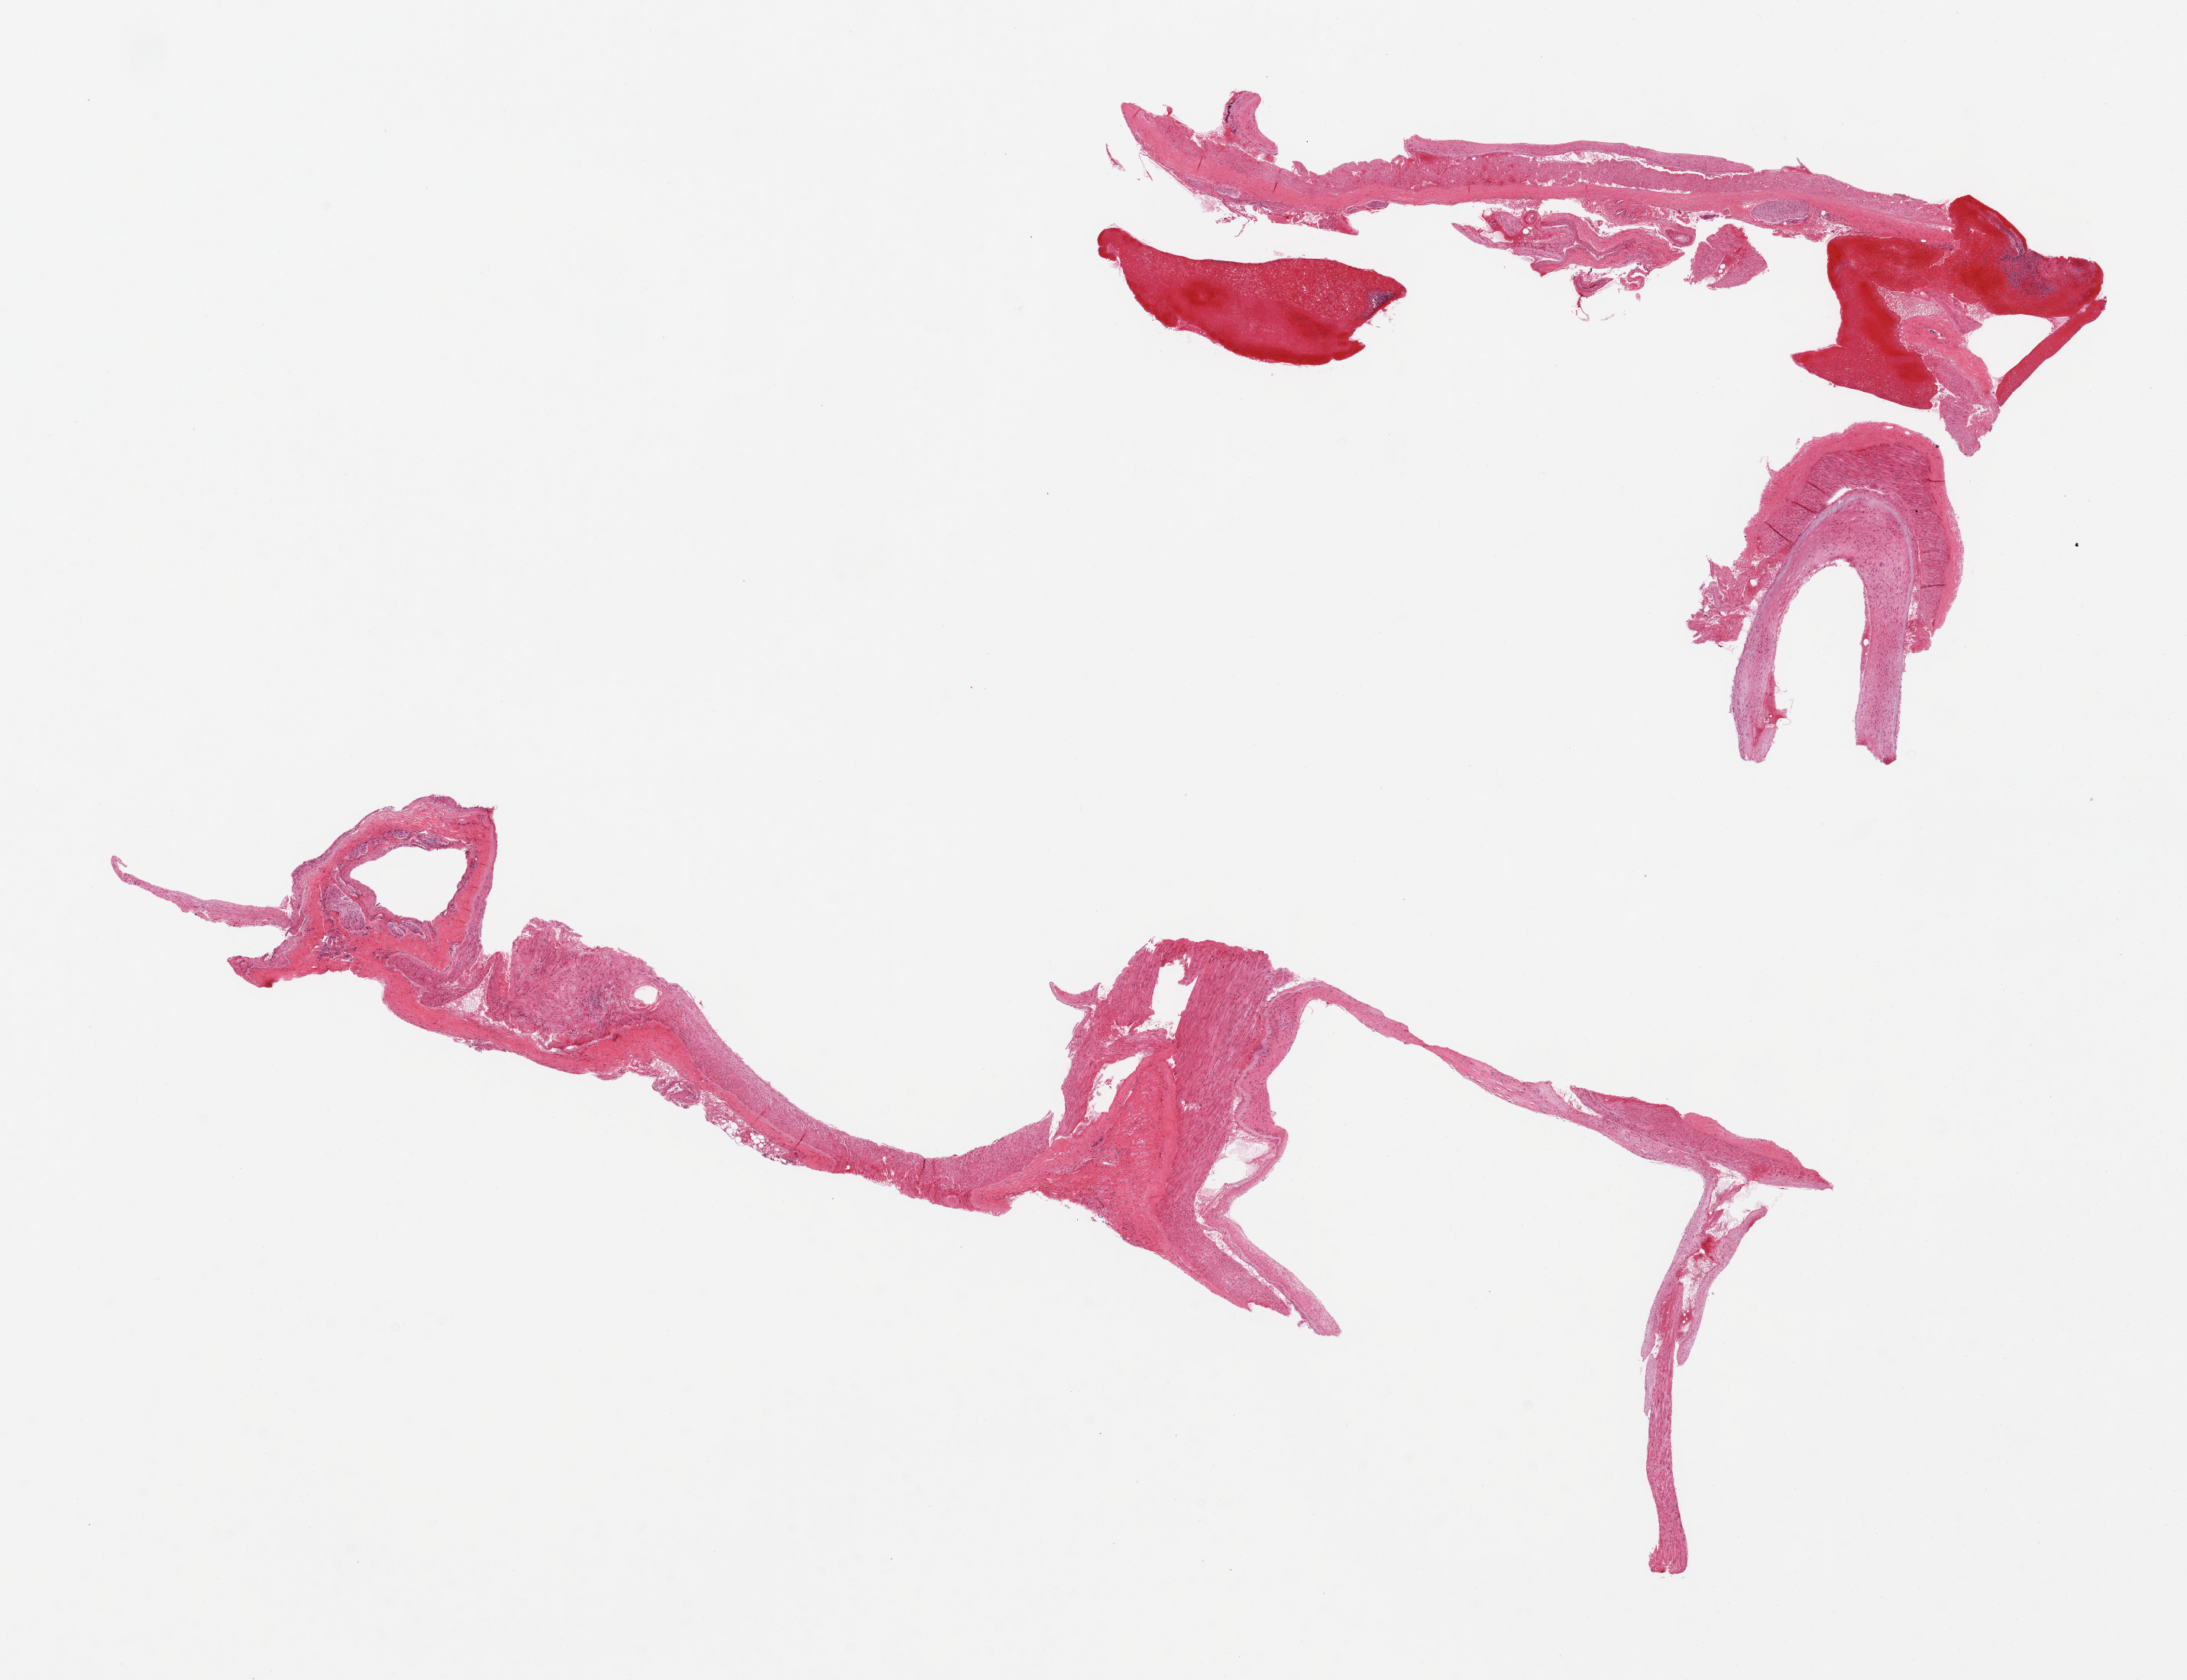
Whole-slide image, haematoxylin and eosin stain, brightfield, low-resolution overview of the scanned area, about 22.6 x 17.4 mm (acquisition: 20x scan); PAXgene-fixed, paraffin-embedded tissue; section of pituitary (target tissue); donor tissue sample. Male donor.
• review note (as recorded): 2 pieces (fragmented)--dura and vascular tissue, no pituitary glandular elements present